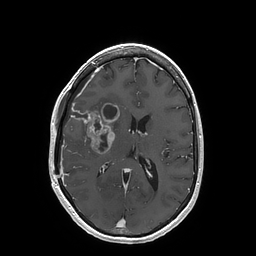
Brain MRI from a brain-tumour surgery series, one axial slice; slice 76 of 202 in the series (ordered by position); T1-weighted post-contrast; 1 mm slice thickness; 256 × 256 image matrix. From the clinical record (not read from this slice): histopathology: Glioblastoma; WHO grade: 4; IDH mutation: no.
Structures marked on this image (outlined manually by an expert reader):
- tumour: bounding box <69,103,119,154> (left, top, right, bottom; pixels)